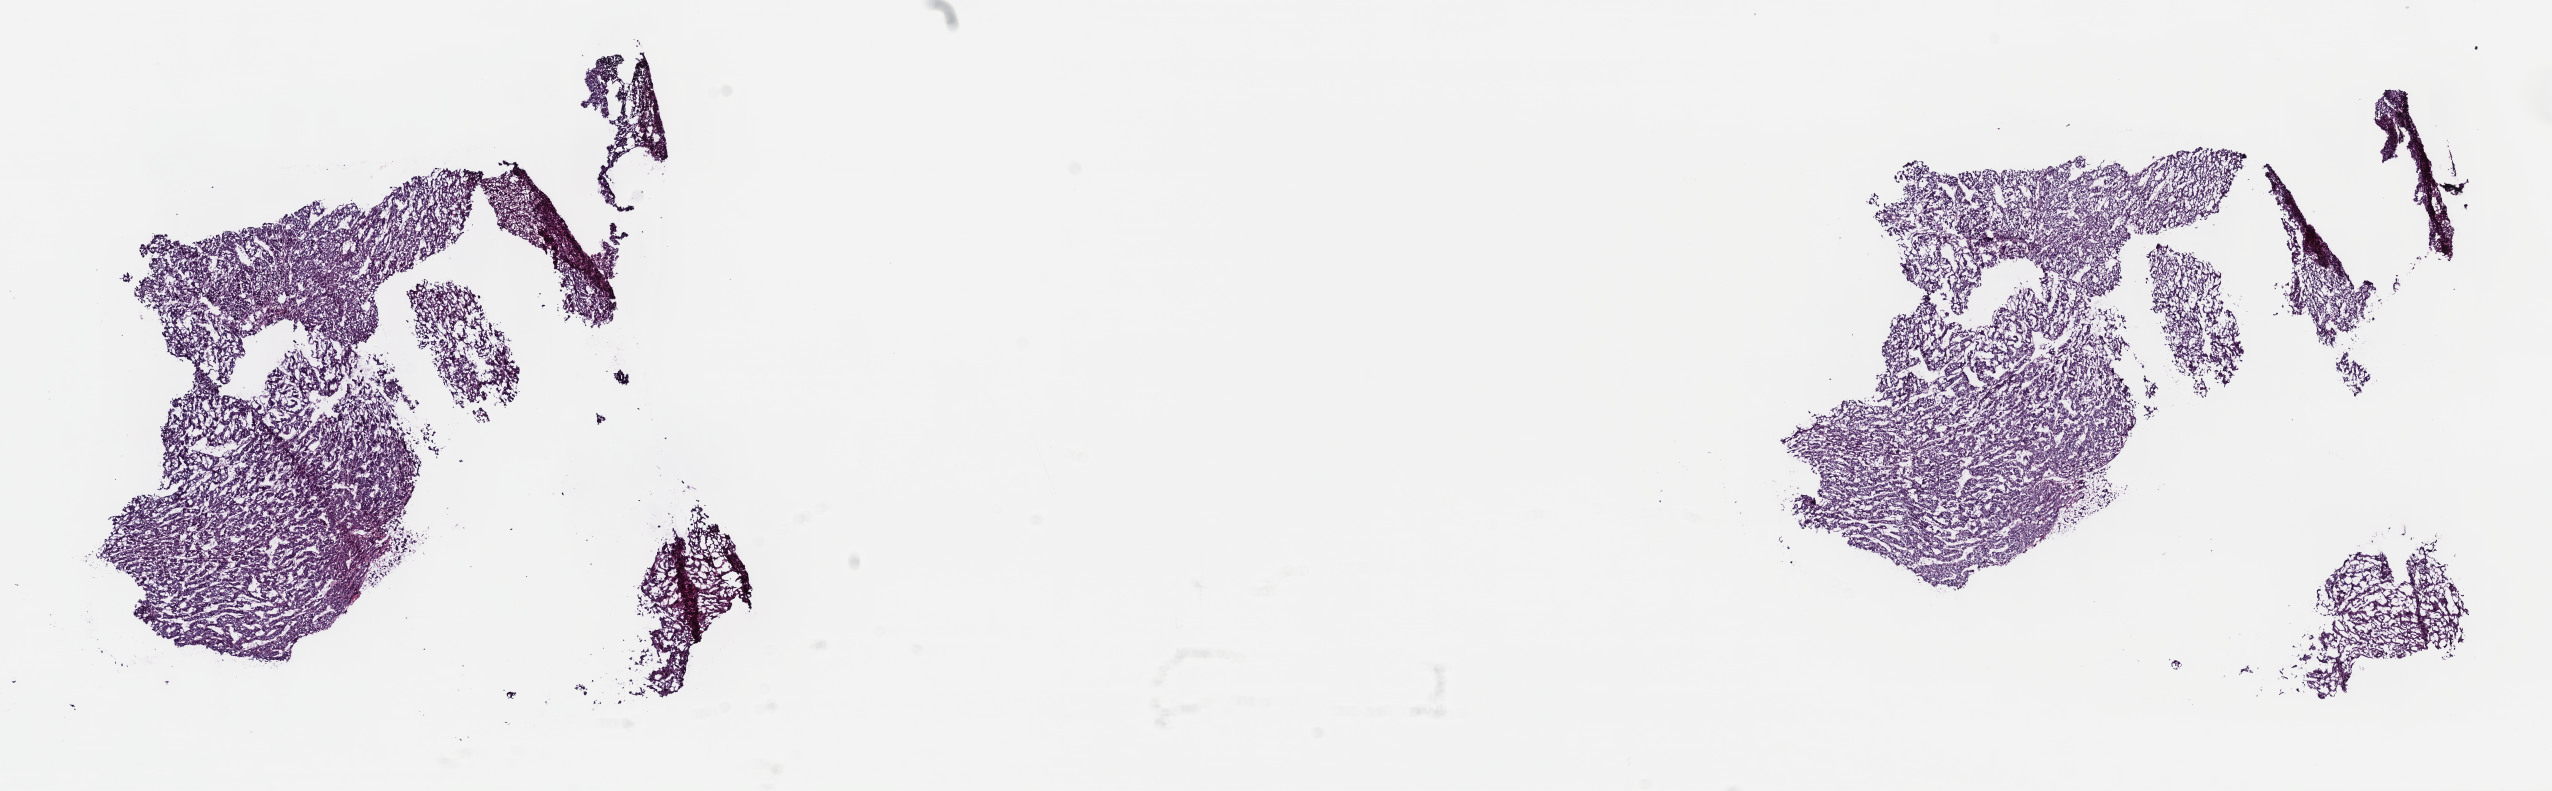
Digitized H&E-stained tissue section (whole slide), a low-resolution overview of the entire scanned area, about 20.6 x 6.4 mm (from a 40x scan); frozen section from the top of the tissue portion; pancreas, primary tumour sample. Male patient; age at initial diagnosis 52 years. Histologic grade: G1 (well differentiated). Composition of this section per pathologist review: tumour cells 80%, tumour nuclei 80%, normal cells 0%, stromal cells 20%, necrosis 0%. Infiltration values recorded for this section: lymphocyte infiltration 70%, monocyte infiltration 10%, neutrophil infiltration 10%.
* TNM: T3 N1 MX
* AJCC pathologic stage: IIB
* diagnosis: Neuroendocrine carcinoma, NOS (head of pancreas)